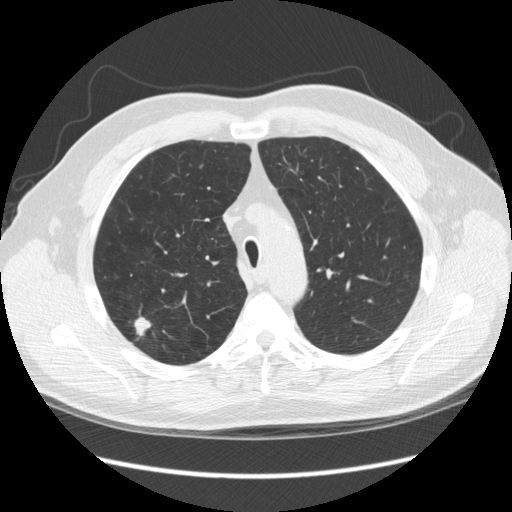
Low-dose screening chest CT, one axial slice; position 187 of 248 along the scan axis; reconstruction kernel STANDARD; 120 kVp; lung window (W 1500 / L -600 HU); 512 × 512 image matrix, field of view 380 × 380 mm.
Annotated regions visible in this slice (expert manual segmentation):
- lesion 1 (tumor, upper lobe of right lung): bounding box <134,317,151,336> (left, top, right, bottom; pixels)